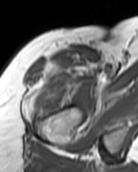
MRI of an extremity soft-tissue mass, one axial slice. Position 84 of 99 along the scan axis. MR volume resampled by the dataset authors to the PET/CT grid (not the native acquisition matrix). 3.27 mm slice thickness. 138 × 172 image matrix, field of view 135 × 168 mm. Female patient. Case-level facts recorded for this patient, not image findings: histological type: pleiomorphic undifferentiated sarcoma; grade: high; site of the primary tumour: right quadricep.
Annotated regions visible in this slice (expert contour drawn on MRI and transferred to this co-registered scan by the dataset authors):
- gross tumour volume including surrounding oedema: box from (x=30, y=79) to (x=81, y=117) px